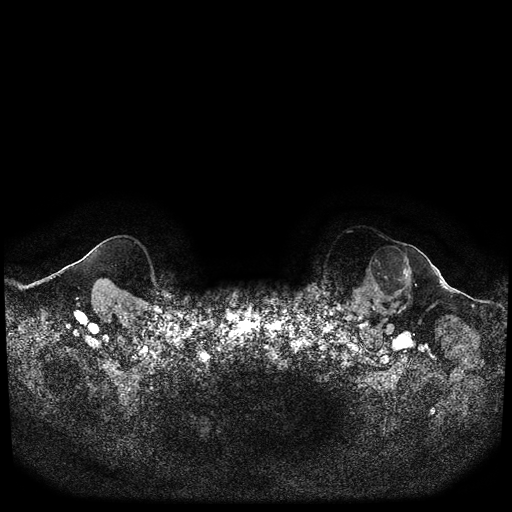
Breast MRI (dynamic contrast-enhanced, multi-phase), one axial slice; slice 101 of 116 in the series (ordered by position); dynamic contrast-enhanced series, time point 2 of 5 at this slice position (early post-contrast); 1.5 T; TE 2.6 ms, TR 5.3 ms; 2 mm slice thickness; 512 × 512 image matrix, field of view 350 × 350 mm. Patient: female, 64 years.
Annotated regions visible in this slice (semi-automatically segmented with operator editing):
- breast lesion (labelled 'tumour' in the annotation; benign lesions carry a separate 'benign' label): bounding box (x1, y1, x2, y2) in pixels: (364, 241, 416, 304)